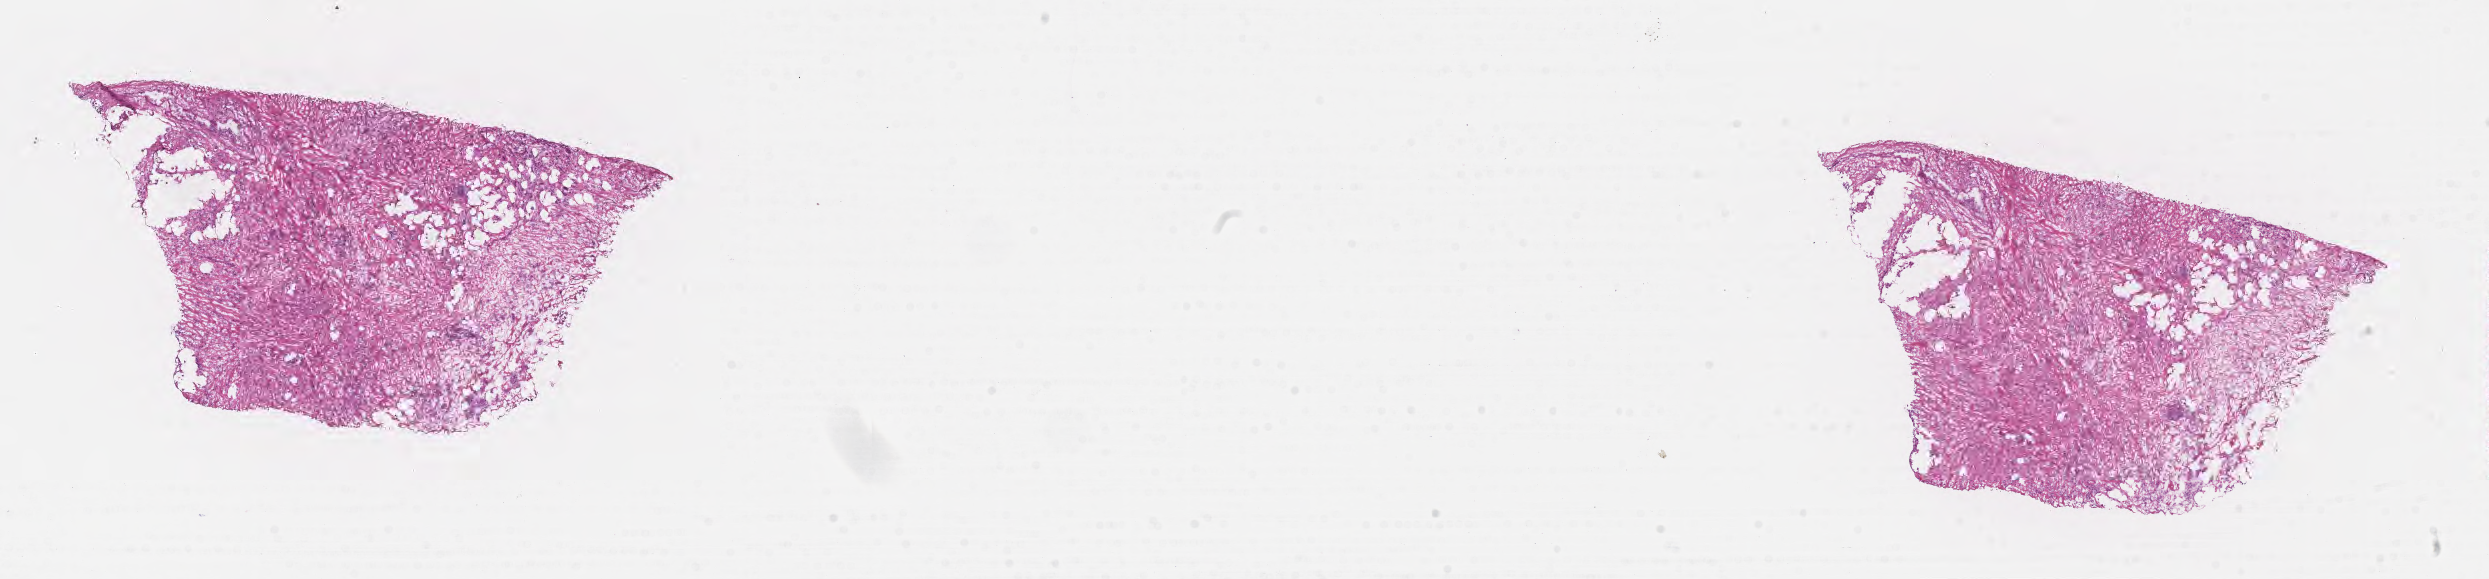
Whole-slide image, hematoxylin and eosin (H&E) stain, low-resolution overview of the scanned area, about 20.1 x 4.7 mm; frozen section (tissue freezing medium); specimen: primary tumor; site: breast. Female, age 60 years at initial diagnosis. Tumor grade: G3 (poorly differentiated). Pathologist review of this section (percent, as recorded): tumor cells 15%, tumor nuclei 80%, stromal cells 85%, necrosis 0%, normal cells 0%. Inflammatory infiltration, as recorded: lymphocyte infiltration 12%, monocyte infiltration 0%, neutrophil infiltration 0%.
Histologic diagnosis: Pleomorphic carcinoma. AJCC pathologic stage: Stage IA.